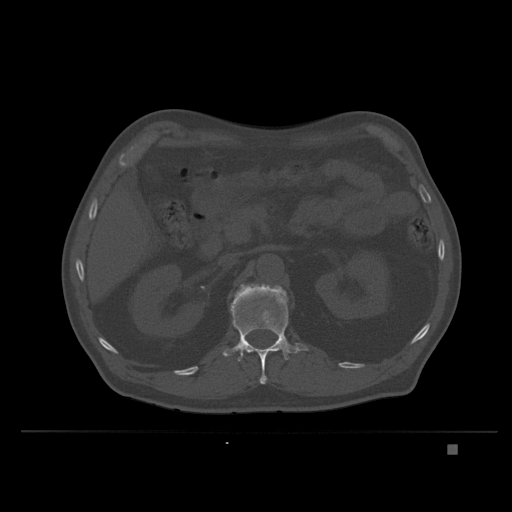
CT including the spine, one axial slice; slice 137 of 435 in the series (ordered by position); bone window (W 1800 / L 400 HU); 1.5 mm slice thickness; 512 × 512 image matrix, field of view 434 × 434 mm. Patient: male, 73 years. Case-level facts recorded for this patient, not image findings: primary cancer: skin.
Structures marked on this image (semi-automatically segmented with operator editing):
- L1 vertebra: bounding box [x1, y1, x2, y2] px = [221, 284, 309, 384]